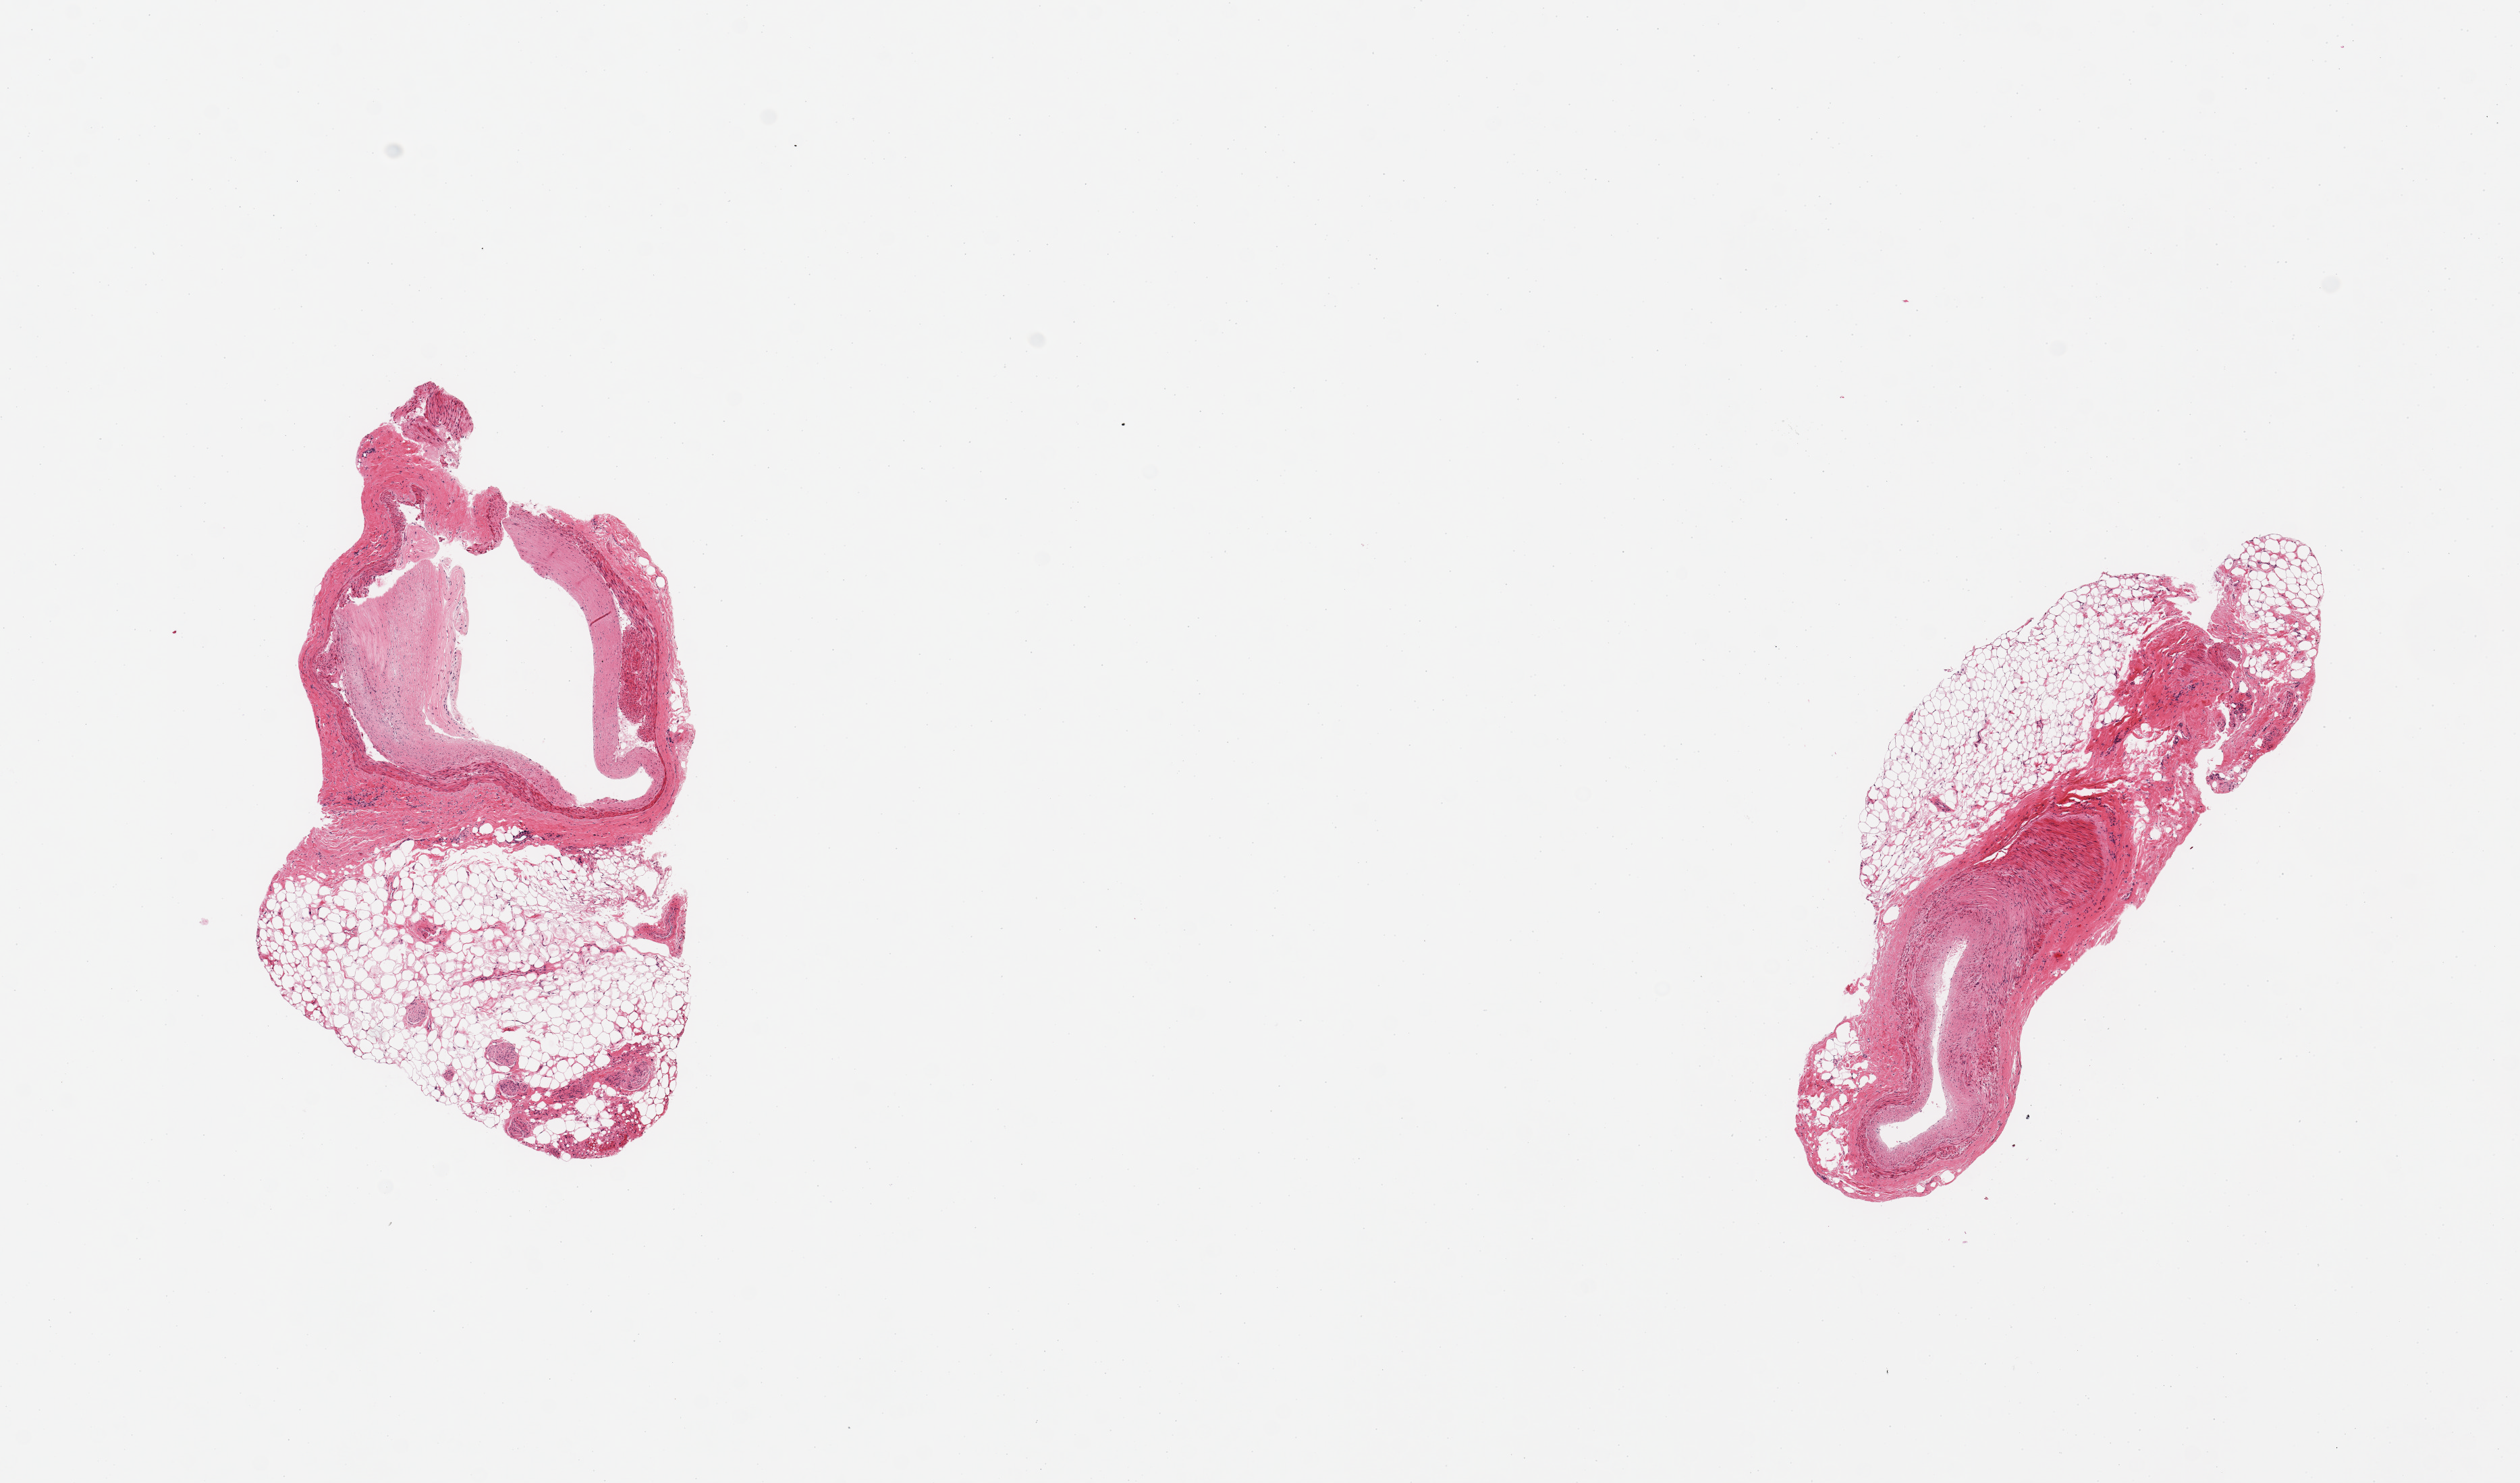
Digitized H&E-stained section — low-resolution overview of the scanned area, about 14.8 x 8.7 mm, PAXgene-fixed, paraffin-embedded tissue, sampled site (target tissue): coronary artery, tissue donor sample. Donor: female.
Pathologist's review note for this sample: 2 pieces; large fibrous plaque in 1; fibrotic wall in other; 50% external fat.